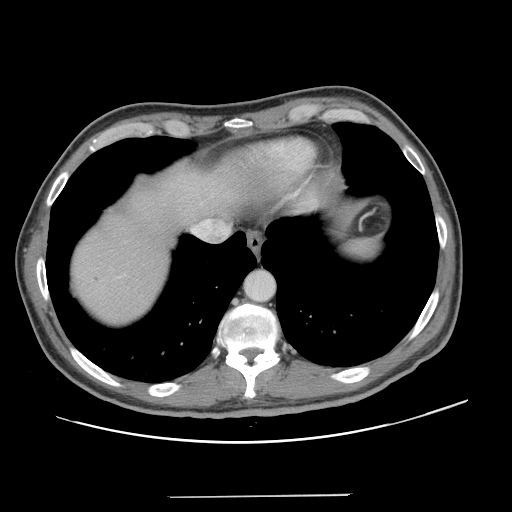
Contrast-enhanced abdominal CT, one axial slice; slice 117 of 131 in the series (ordered by position); 120 kVp; intravenous contrast given; soft-tissue window (W 400 / L 40 HU); 2.5 mm slice thickness; 512 × 512 image matrix. Male patient, age 60 years. From the clinical record (not read from this slice): diagnosis: colorectal cancer liver metastases, imaged before liver resection; multiple liver metastases: no; largest metastasis: 2.5 cm; chemotherapy before resection: no.
Annotated regions visible in this slice (manually delineated by an expert):
- hepatic veins: bounding box <191,219,216,240> (left, top, right, bottom; pixels)
- liver: <69,141,310,326>
- planned liver remnant (the part of the liver to remain after resection): <71,143,309,324>